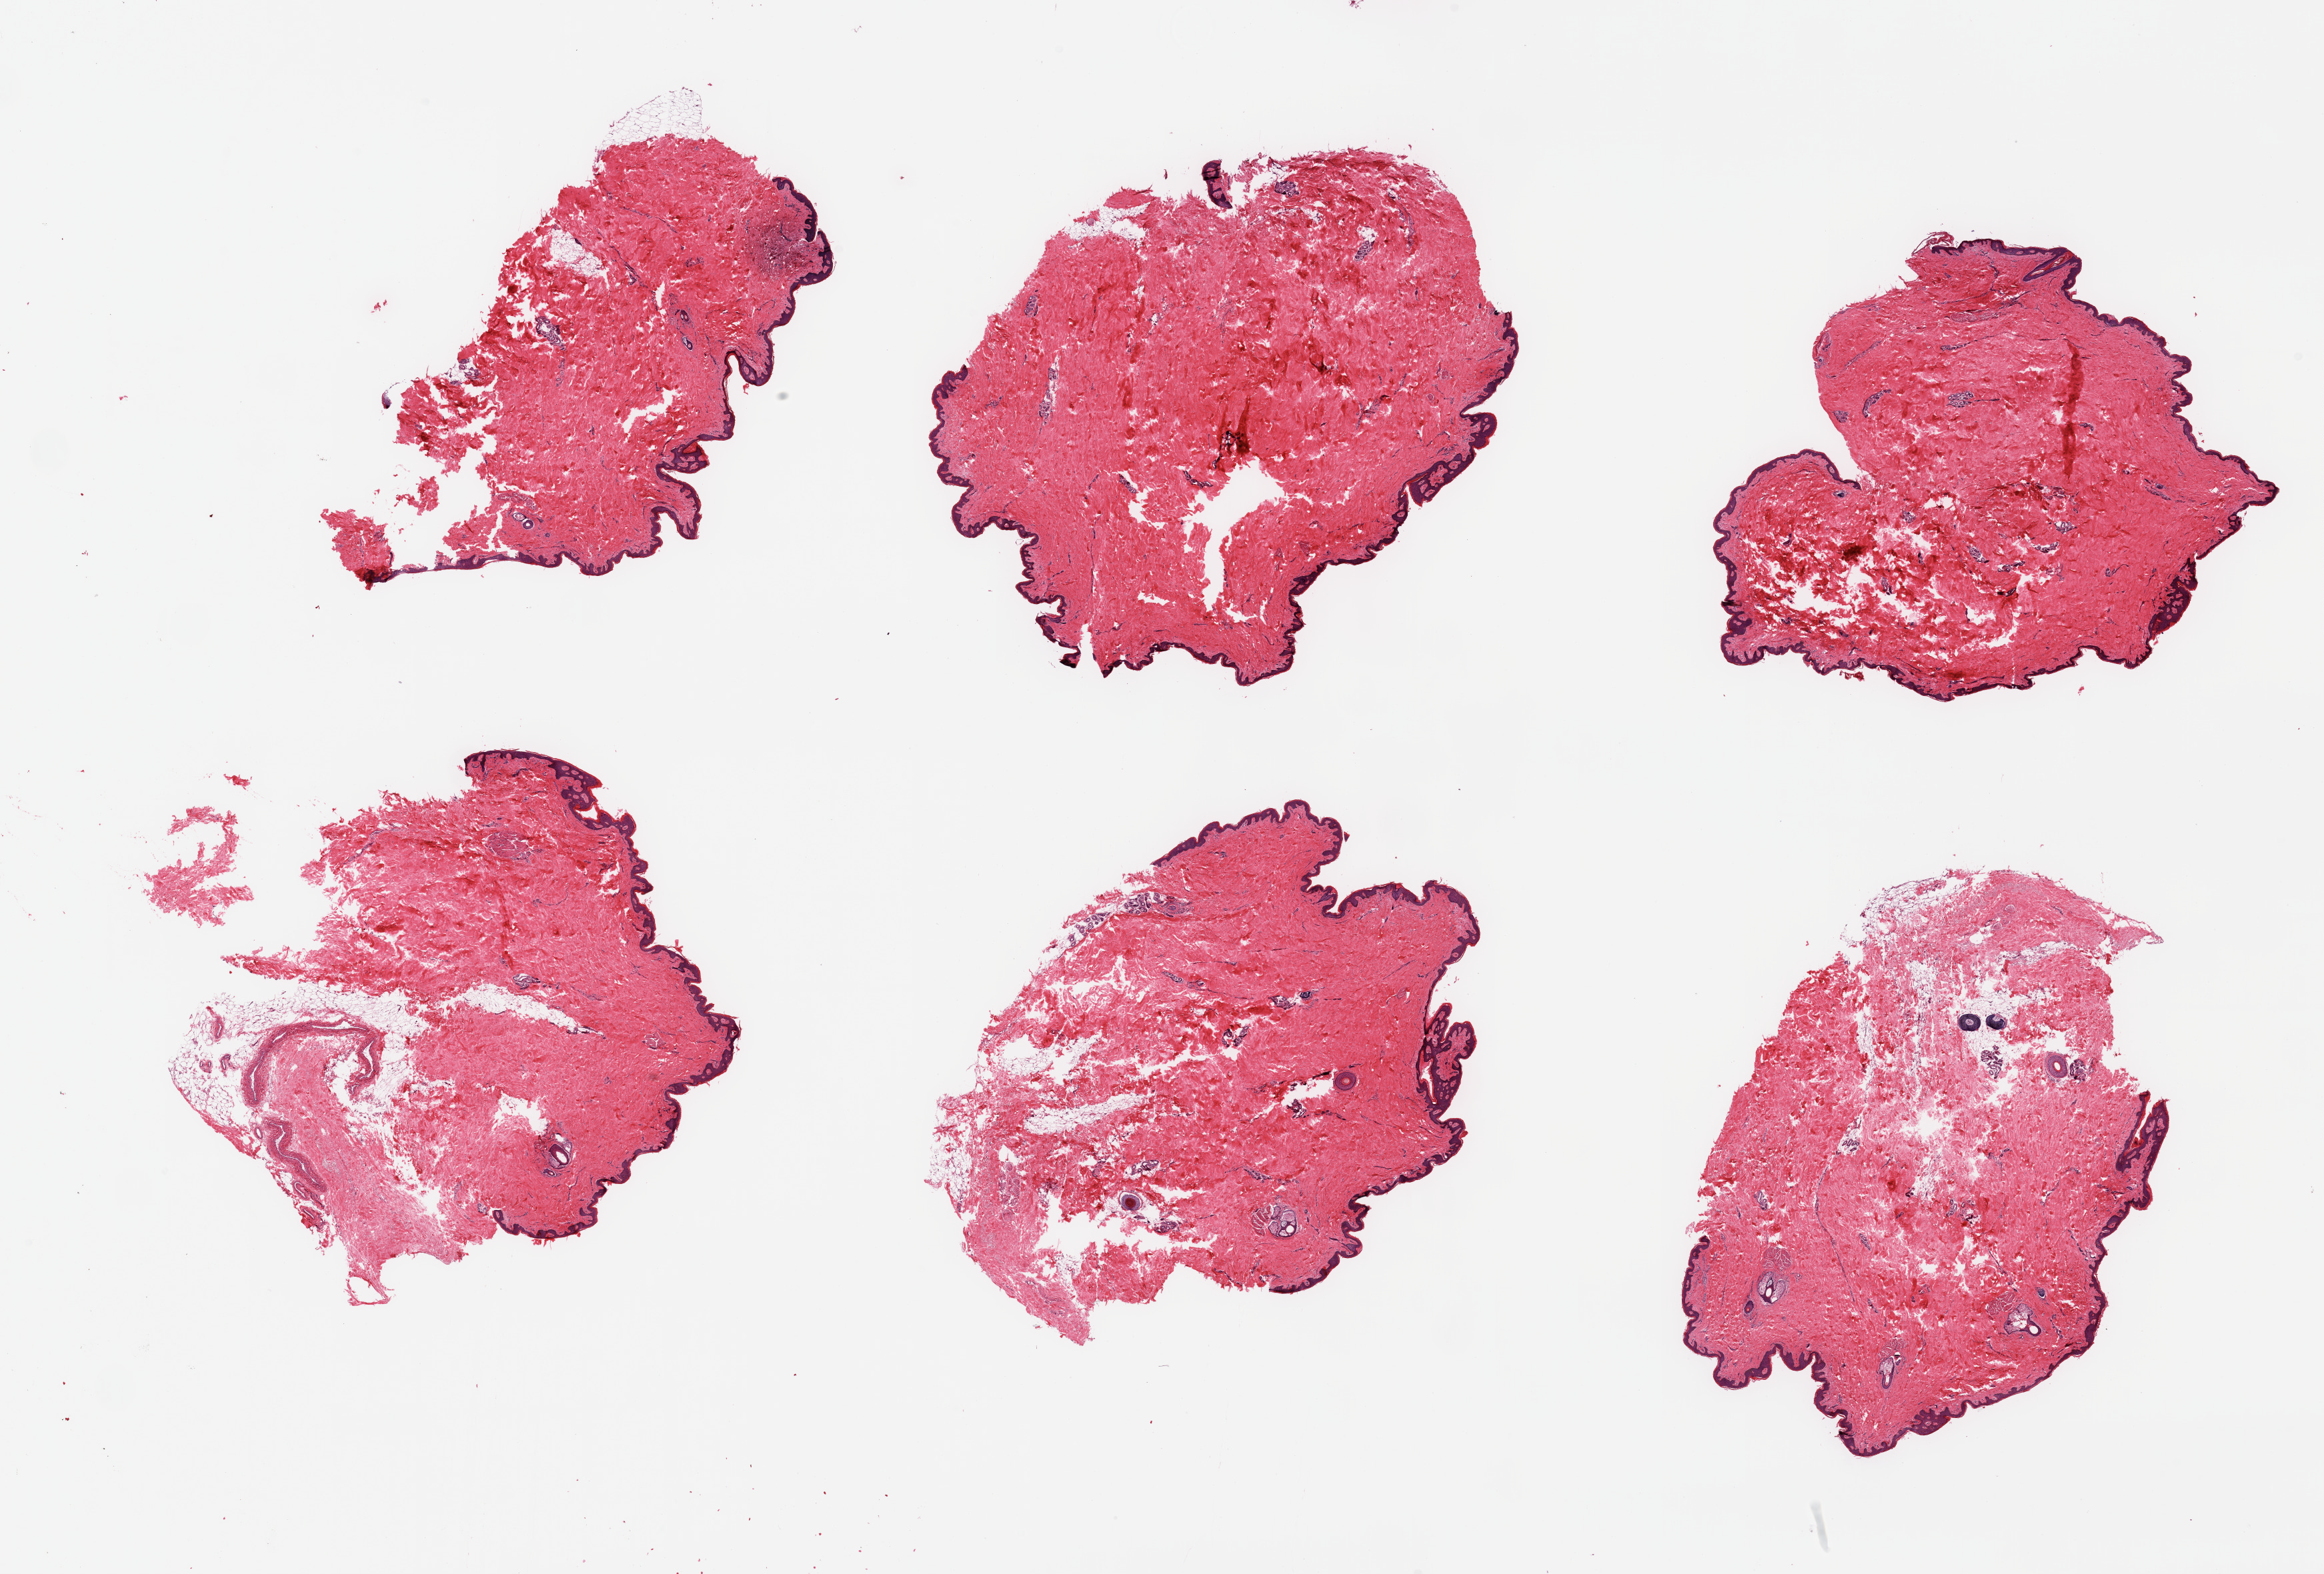
Whole-slide image, hematoxylin and eosin (H&E) stain — whole scanned area (about 27.6 x 18.7 mm) shown as a low-resolution overview, PAXgene-fixed paraffin-embedded (PFPE) section, section of skin of suprapubic region (target tissue), tissue donor sample. Donor: male.
Reviewer comment on this tissue sample: 6 pieces, no signficant adherent dermal fat; squamous epithelium is ~70 microns.